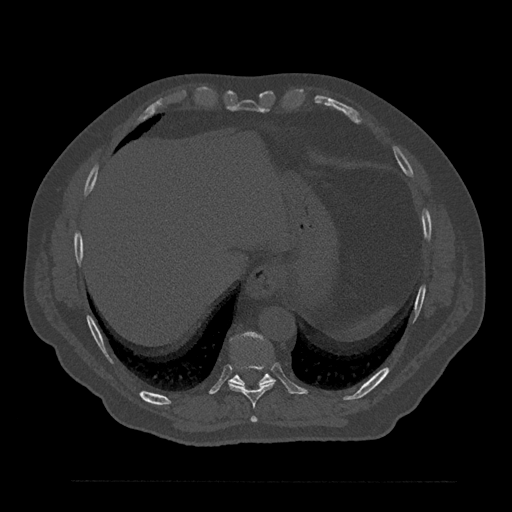
CT including the spine, one axial slice. Slice 385 of 797 in the series (ordered by position). Reconstruction kernel Br40s/3. 120 kVp. Bone window (W 1800 / L 400 HU). 512 × 512 image matrix, field of view 430 × 430 mm. Male patient, age 61 years. From the clinical record (not read from this slice): primary cancer: prostate.
Structures marked on this image (semi-automatically segmented with operator editing):
- T10 vertebra: bounding box <228,332,274,386> (left, top, right, bottom; pixels)
- T8 vertebra: <251,416,257,423>
- T9 vertebra: <228,365,275,408>